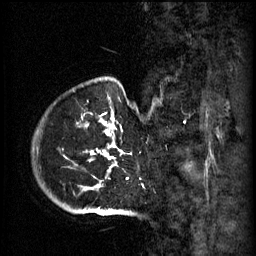
Breast MRI (dynamic contrast-enhanced), one sagittal slice; position 52 of 60 along the scan axis; 3 images stored at this slice position (order not interpretable as contrast timing); 1.5 T; TE 4.2 ms, TR 11 ms; 2 mm slice thickness; 256 × 256 image matrix, field of view 200 × 200 mm. Patient: female, 51 years.
Structures marked on this image (semi-automatically segmented with operator editing):
- analysis volume of interest (the breast-tissue region the enhancement analysis was run in; not a lesion): box from (x=48, y=82) to (x=159, y=197) px
- tumour enhancement mask (voxels above the 70 % enhancement threshold inside the analysis volume of interest): (x=93, y=114)–(x=129, y=183)